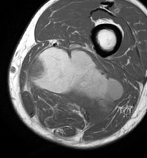
MRI of an extremity soft-tissue mass, one axial slice; slice 35 of 86 in the series (ordered by position); MR volume resampled by the dataset authors to the PET/CT grid (not the native acquisition matrix); 147 × 158 image matrix, field of view 144 × 154 mm. Male patient. From the clinical record (not read from this slice): histological type: undifferentiated pleomorphic liposarcoma; grade: high; site of the primary tumour: left thigh.
Annotated regions visible in this slice (expert contour drawn on MRI and transferred to this co-registered scan by the dataset authors):
- gross tumour volume including surrounding oedema: bounding box <25,40,124,127> (left, top, right, bottom; pixels)
- gross tumour volume (mass): <25,47,124,127>